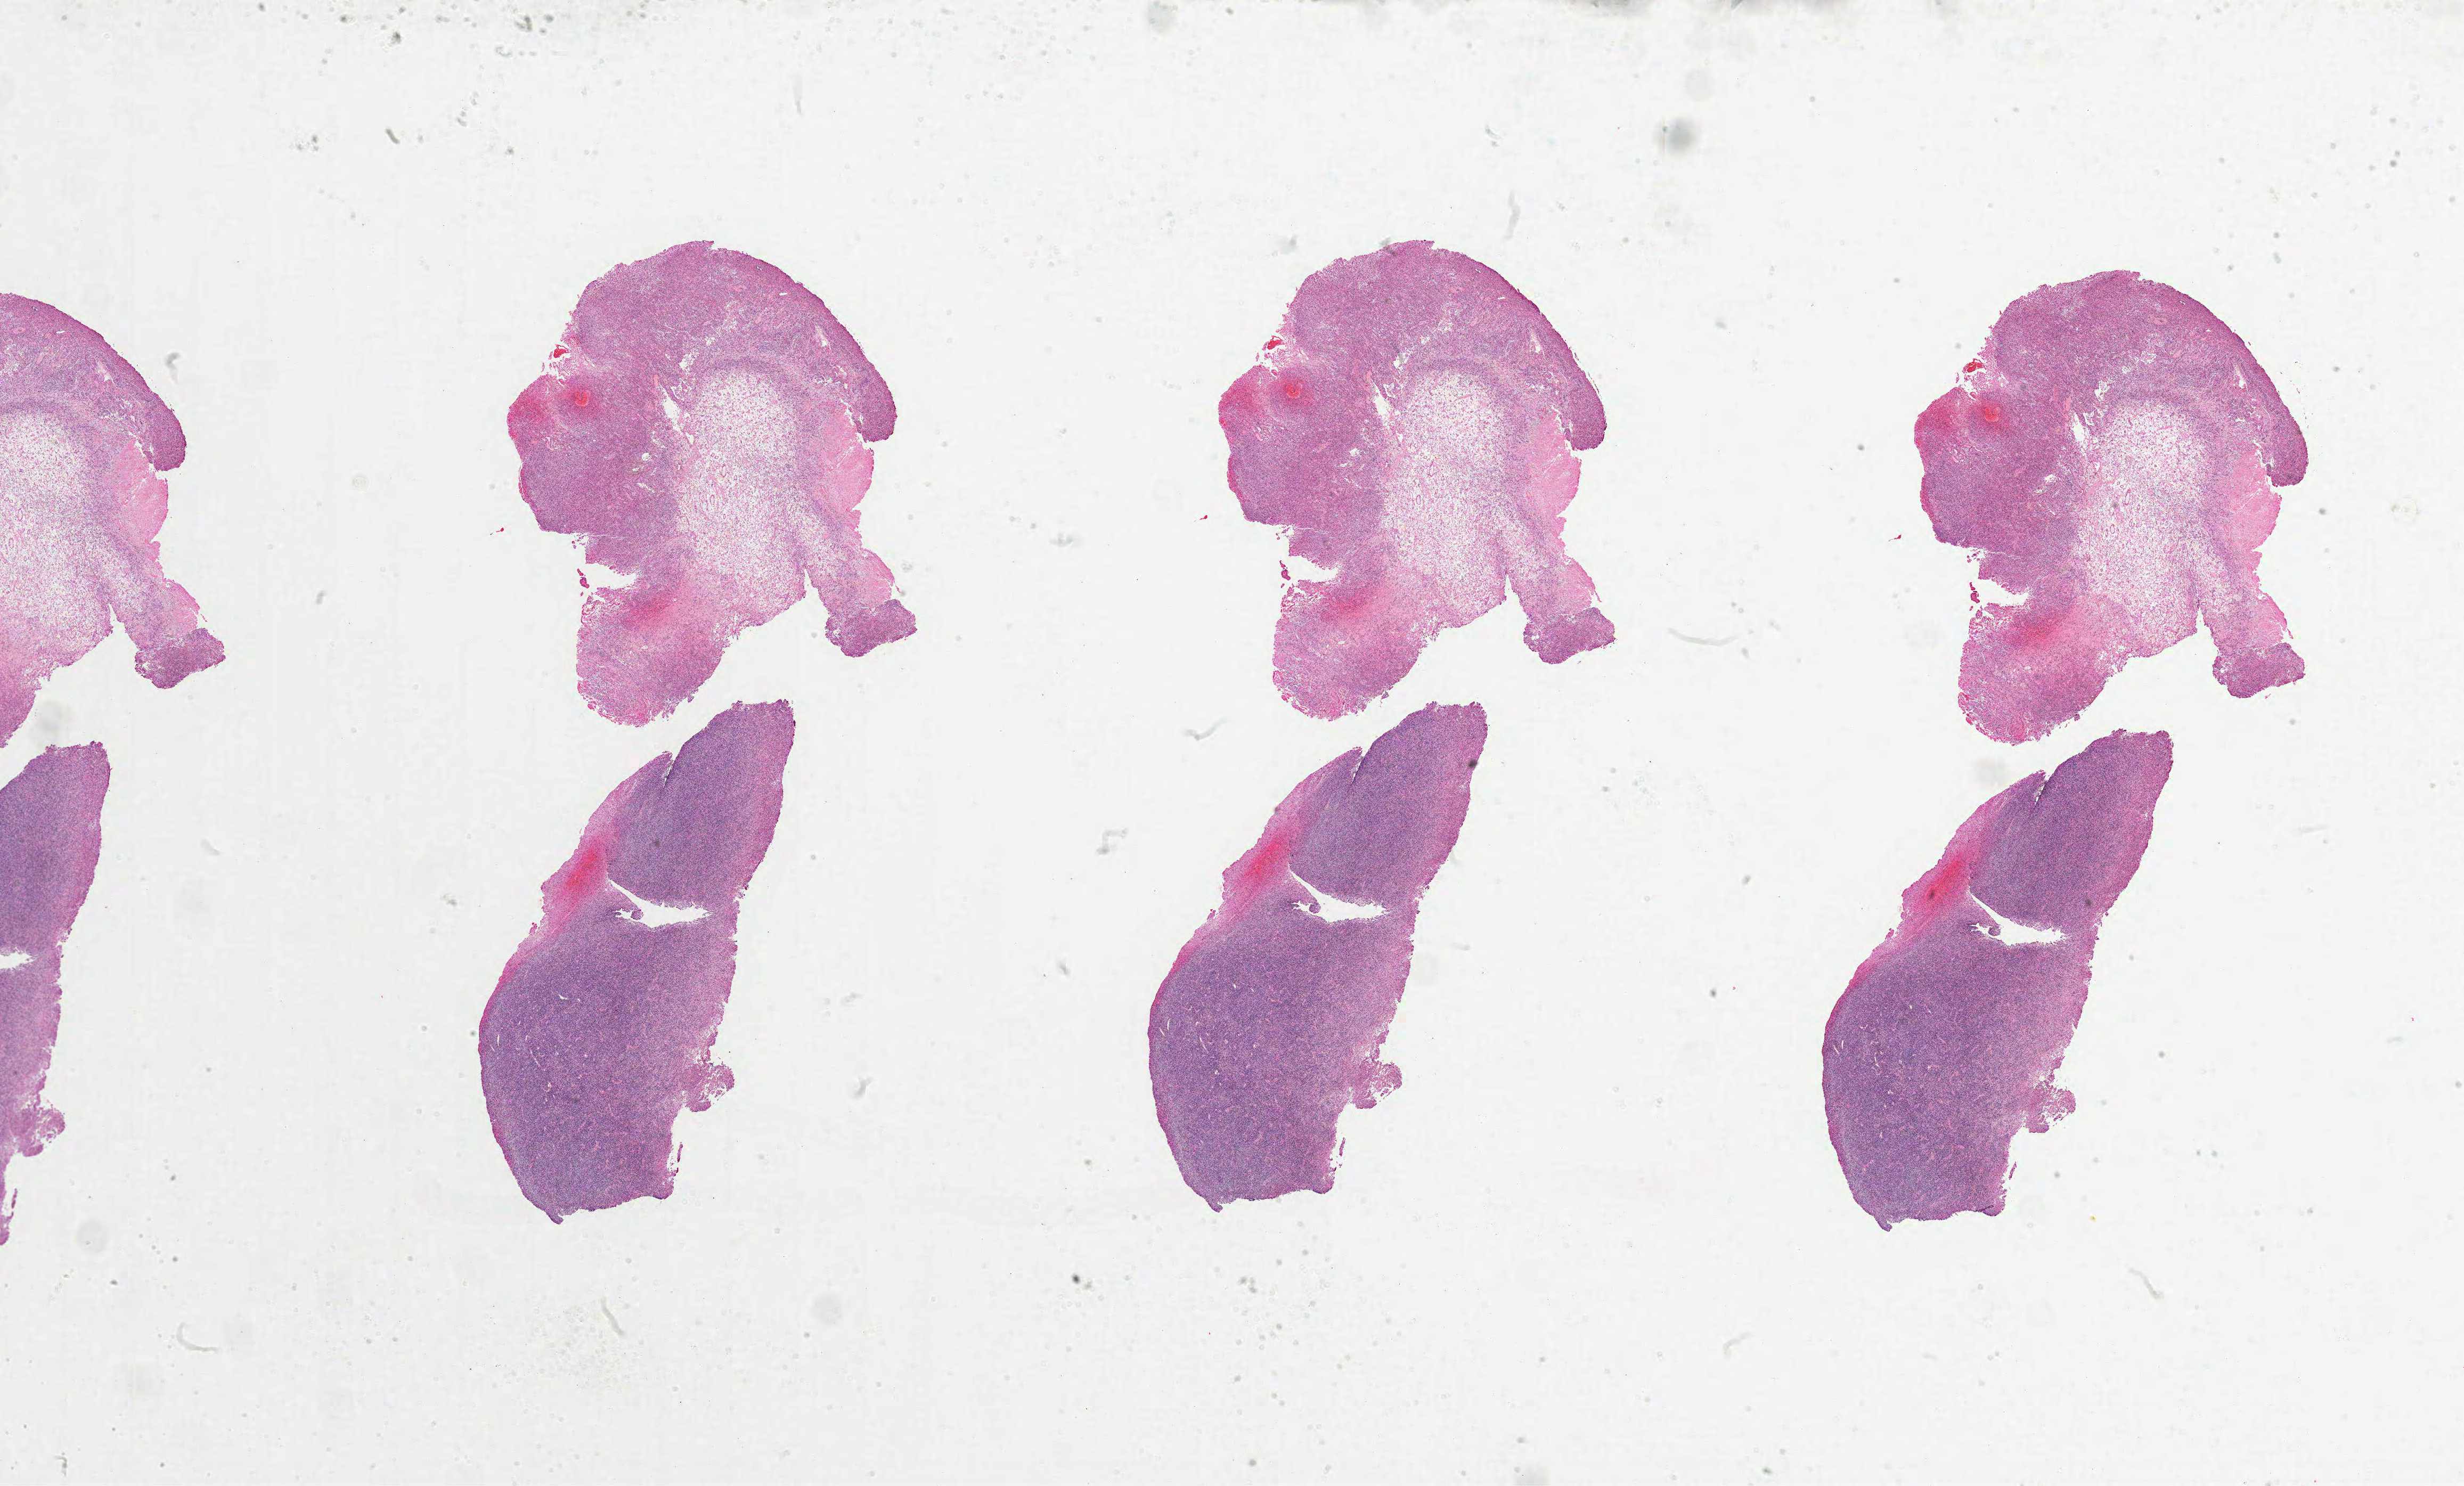
H&E whole-slide image — low-resolution overview of the scanned area, about 37.0 x 22.3 mm (slide scanned at 20x). Formalin-fixed paraffin-embedded (FFPE) diagnostic section. Brain, primary tumour sample. Patient: male, age at initial diagnosis 69 years.
Histologic diagnosis: Glioblastoma.